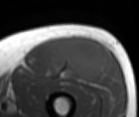
MRI of an extremity soft-tissue mass, one axial slice. Slice 45 of 86 in the series (ordered by position). MR volume resampled by the dataset authors to the PET/CT grid (not the native acquisition matrix). 3.27 mm slice thickness. 139 × 117 image matrix. Male patient. Case-level facts recorded for this patient, not image findings: histological type: extraskeletal osteosarcoma; grade: high; site of the primary tumour: thigh.
Structures marked on this image (expert contour drawn on MRI and transferred to this co-registered scan by the dataset authors):
- gross tumour volume (mass): bounding box (x1, y1, x2, y2) in pixels: (52, 36, 105, 81)